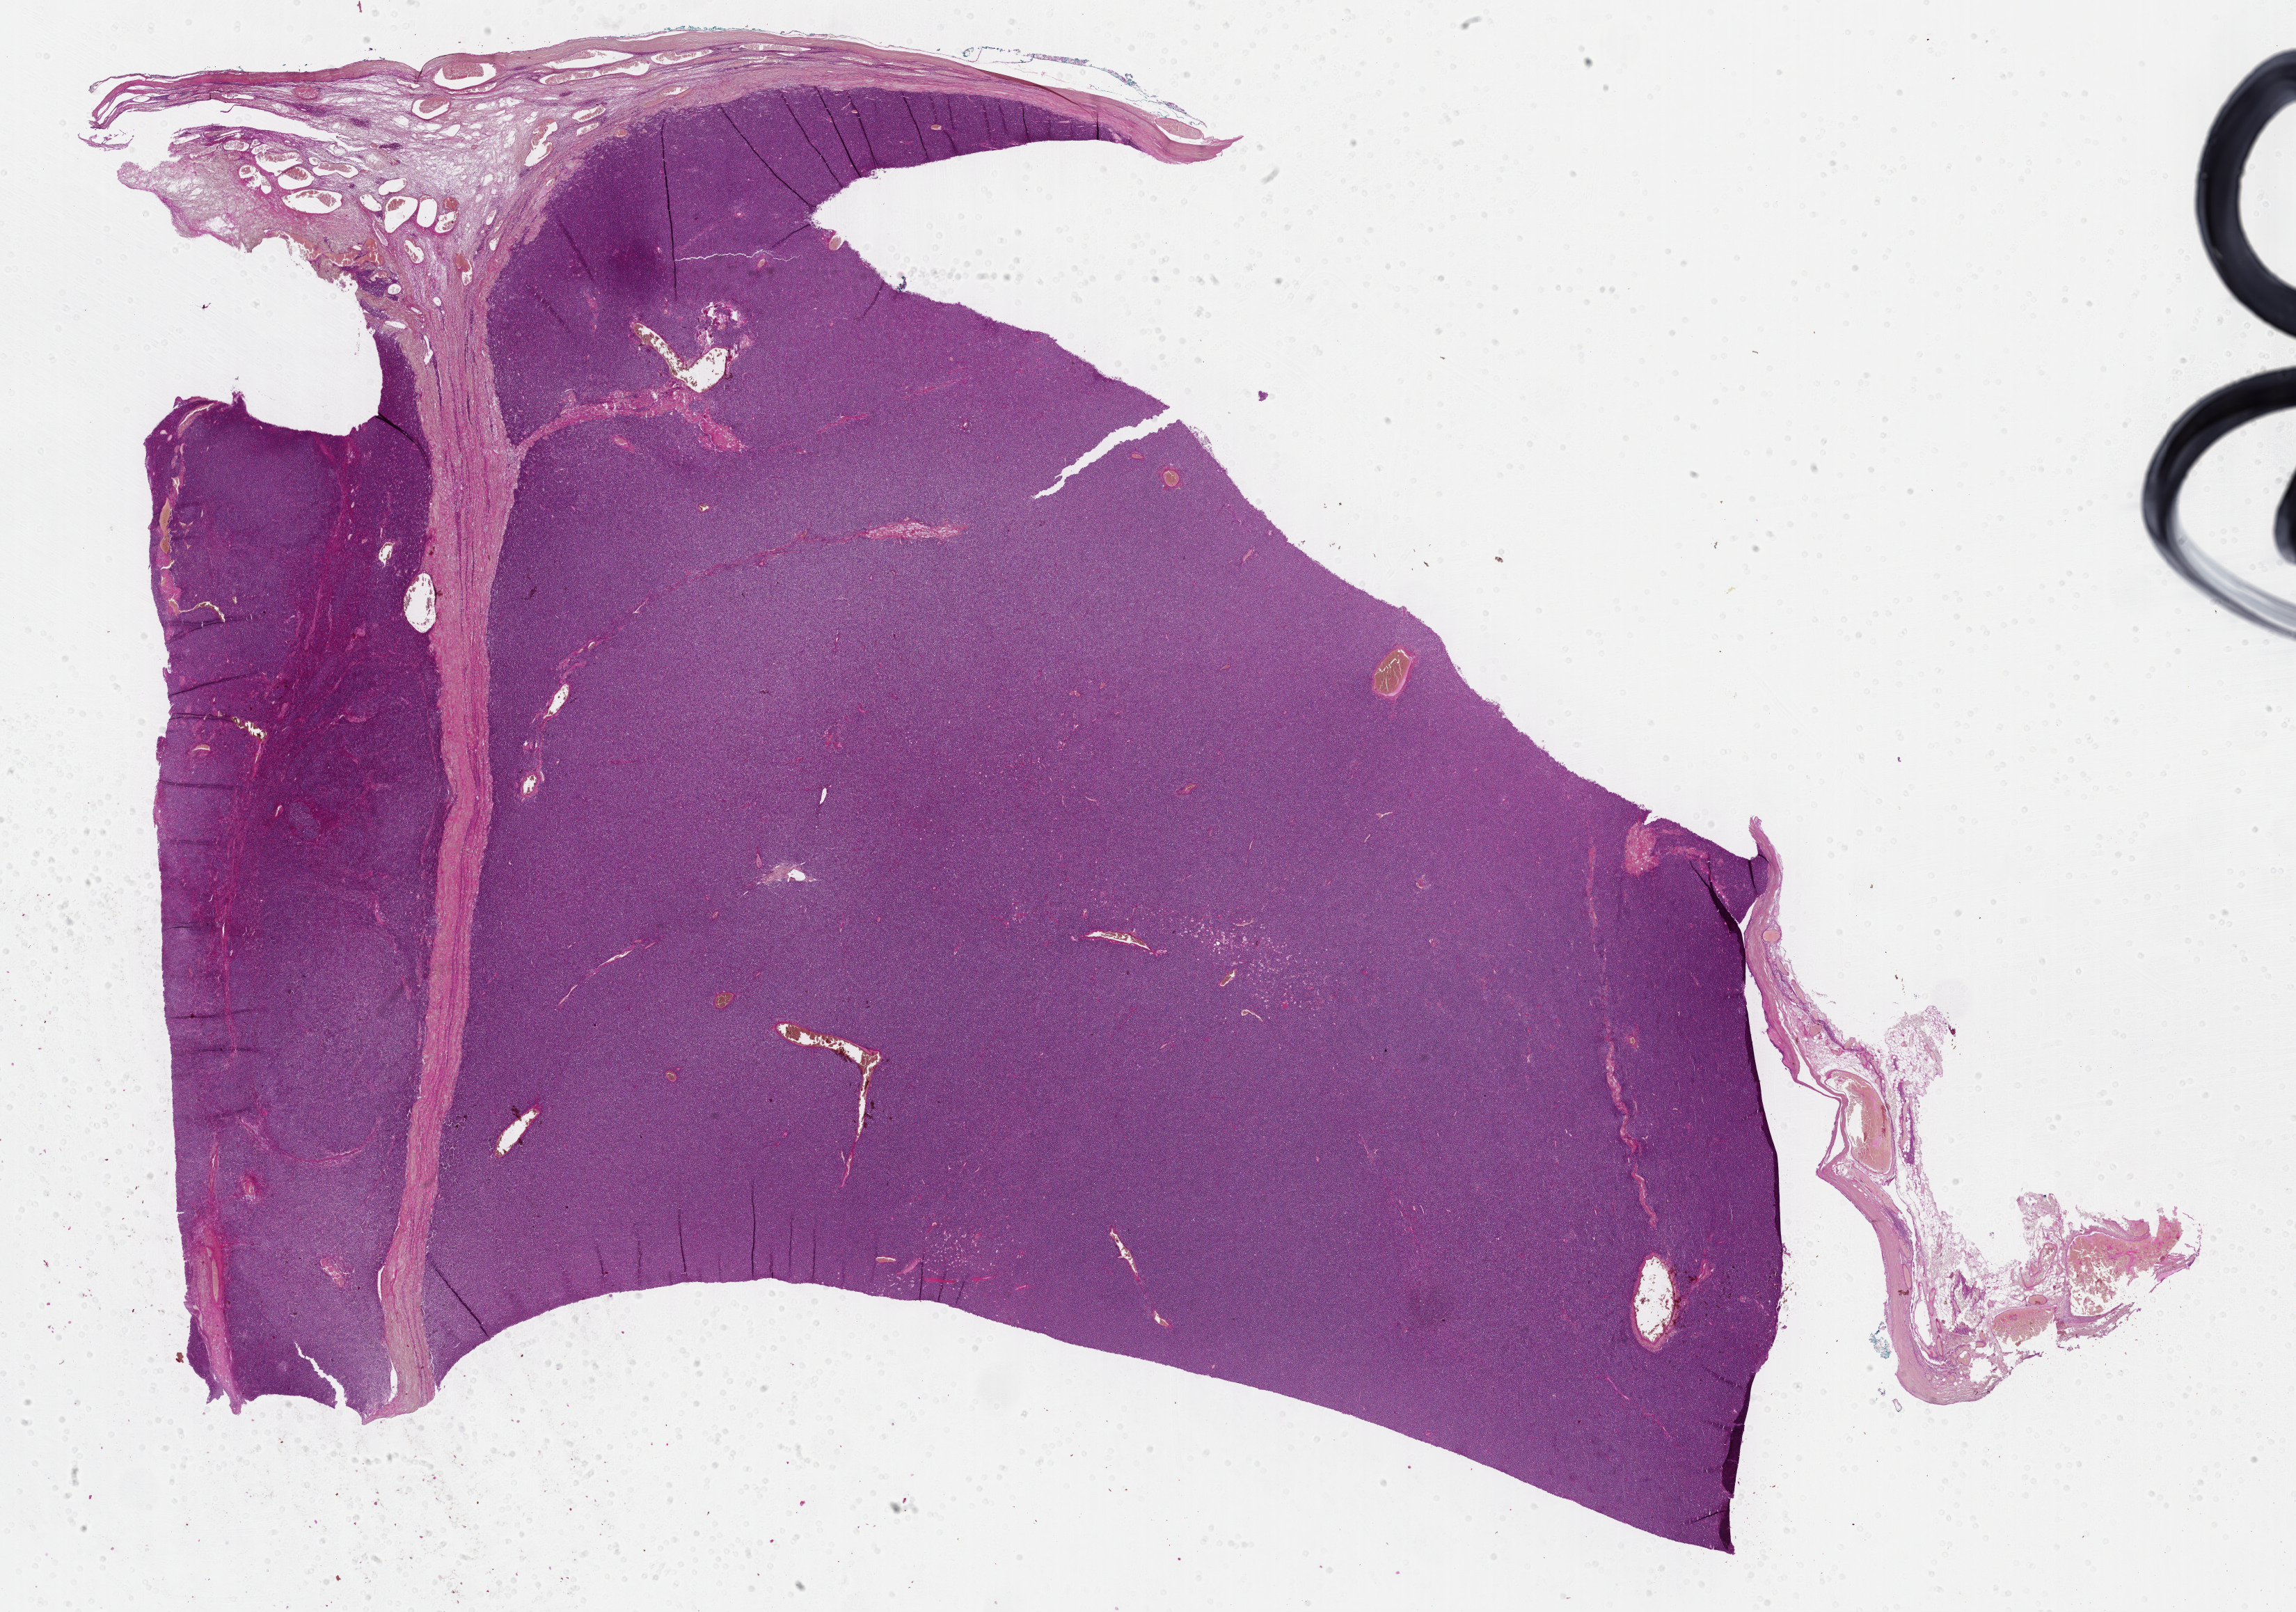
Whole-slide histology image, Hematoxylin and eosin (H&E) stained, shown as a low-resolution overview of the whole scanned area (about 26.7 x 18.7 mm). Formalin-fixed paraffin-embedded (FFPE) diagnostic section. Thymus, primary tumour sample. Male, age 39 years at initial diagnosis.
Diagnosis: Thymoma, type AB, malignant.